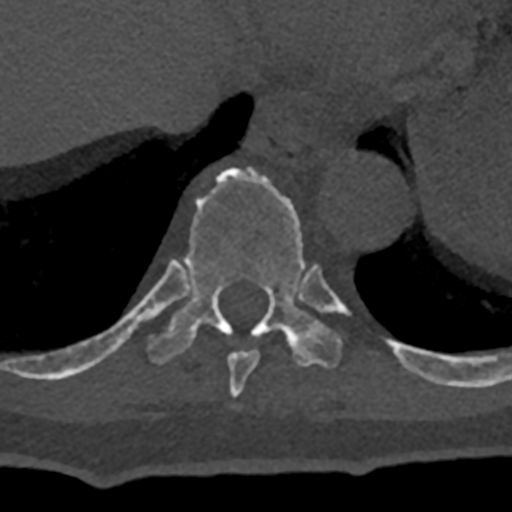
CT including the spine, one axial slice; position 618 of 797 along the scan axis; 120 kVp; bone window (W 1800 / L 400 HU); 0.5 mm slice thickness; 512 × 512 image matrix, field of view 160 × 160 mm. Patient: male, 74 years. Case-level facts recorded for this patient, not image findings: primary cancer: renal; vertebrae with lytic lesions (as recorded): T10, L1, L2, L3, L4, L5.
Structures marked on this image (semi-automatic segmentation, software-assisted and operator-edited):
- T10 vertebra: bounding box (x1, y1, x2, y2) in pixels: (70, 166, 432, 382)
- T9 vertebra: (228, 350, 259, 398)